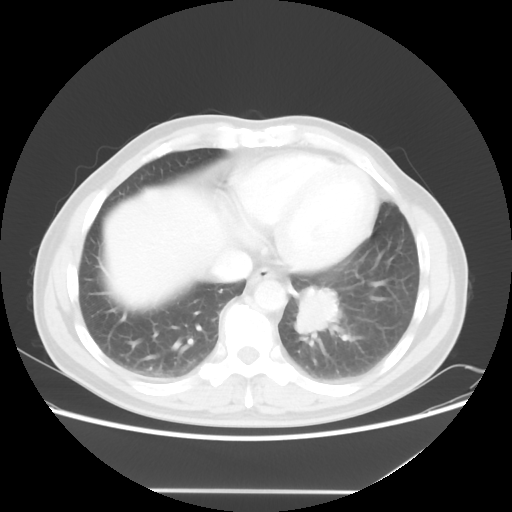
Chest CT, one axial slice. Slice 17 of 56 in the series (ordered by position). Reconstruction kernel STANDARD. 120 kVp. Lung window (W 1500 / L -600 HU). 512 × 512 image matrix, field of view 385 × 385 mm. Patient: male, 61 years. Case-level facts recorded for this patient, not image findings: clinical TNM (as recorded): T1c N0 M0.
Structures marked on this image (rectangle marked by the reading radiologist):
- lung tumour (recorded histology: adenocarcinoma): bounding box <286,284,345,341> (left, top, right, bottom; pixels)